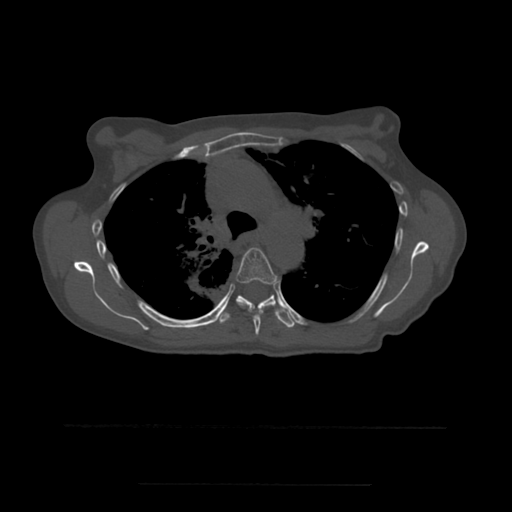
CT including the spine, one axial slice; position 386 of 544 along the scan axis; bone window (W 1800 / L 400 HU); 1.25 mm slice thickness; 512 × 512 image matrix. Patient age 58 years. Case-level facts recorded for this patient, not image findings: primary cancer: lung.
Annotated regions visible in this slice (semi-automatically segmented with operator editing):
- T5 vertebra: box from (x=236, y=248) to (x=278, y=336) px
- T6 vertebra: (x=218, y=295)–(x=296, y=328)